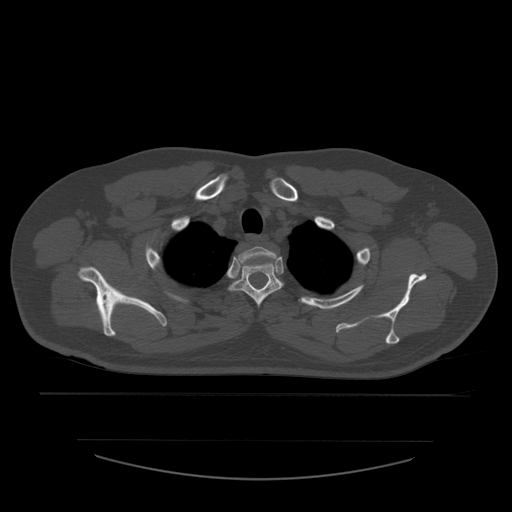
CT including the spine, one axial slice. Slice 453 of 532 in the series (ordered by position). 120 kVp. Bone window (W 1800 / L 400 HU). 512 × 512 image matrix. Patient age 44 years. From the clinical record (not read from this slice): primary cancer: soft tissue sarcoma.
Annotated regions visible in this slice (semi-automatic segmentation, software-assisted and operator-edited):
- T1 vertebra: bounding box [x1, y1, x2, y2] px = [237, 247, 277, 269]
- T2 vertebra: [229, 263, 283, 308]